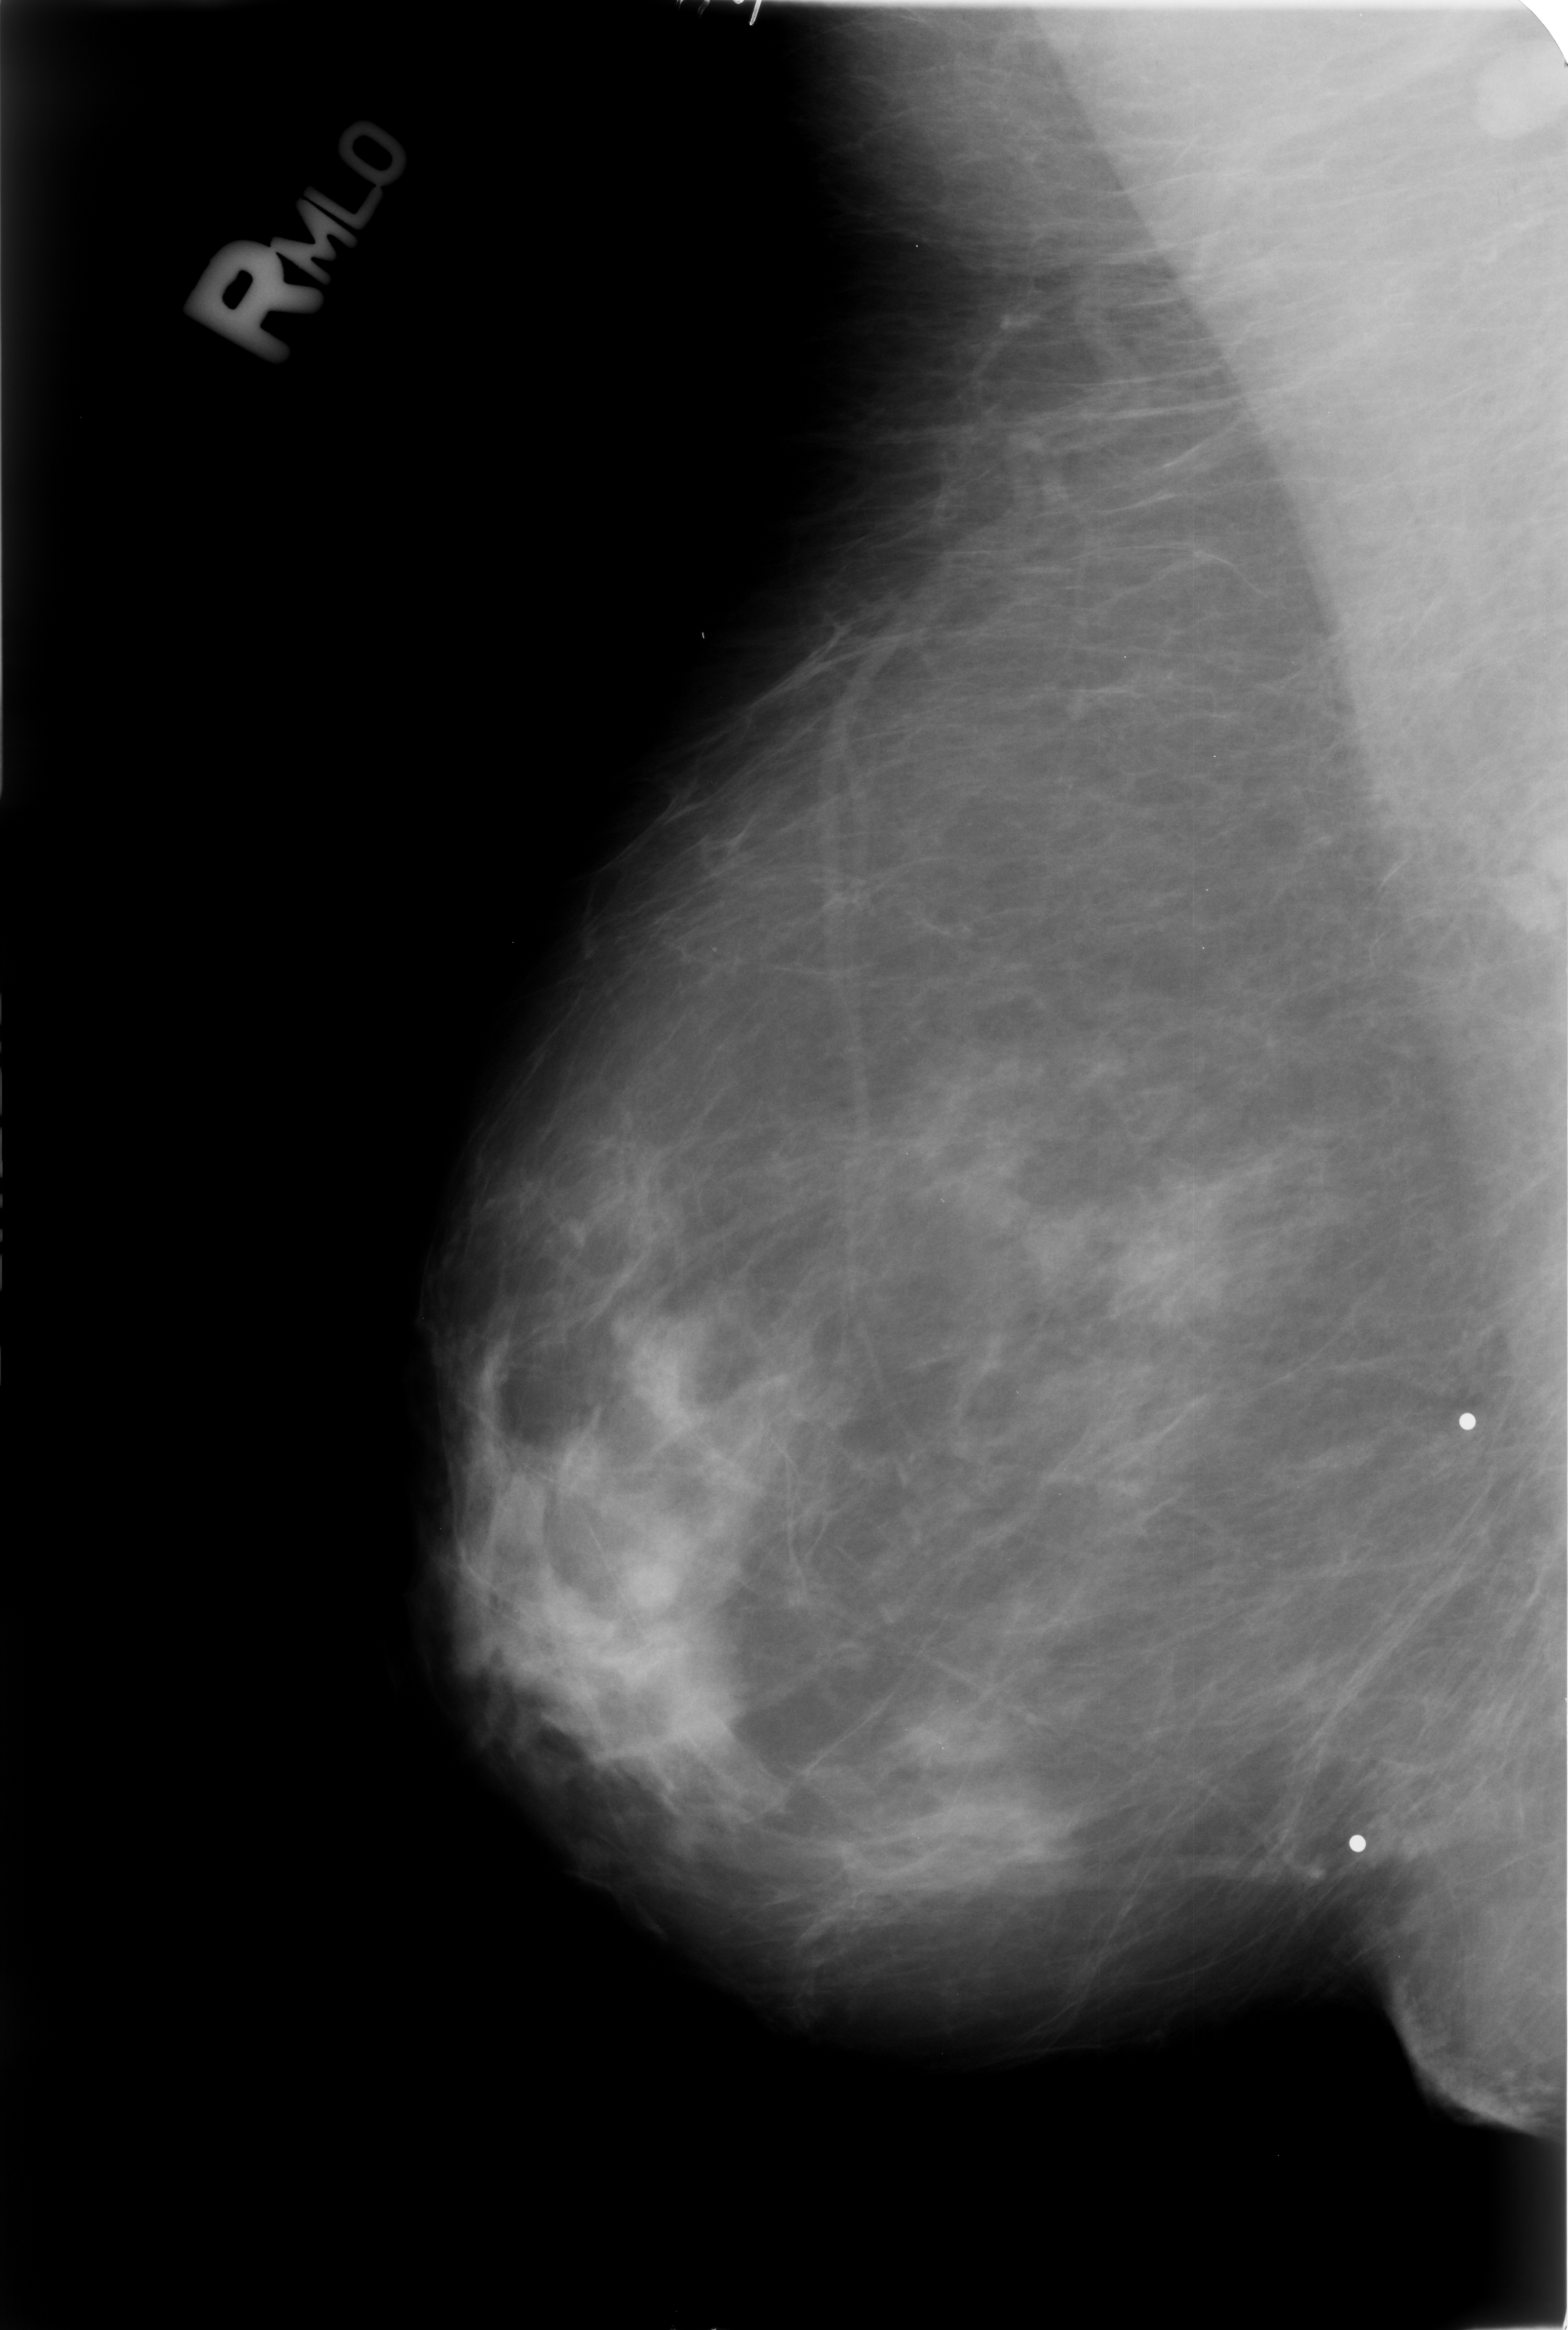
Scanned film-screen mammogram. Right breast. MLO view. Breast composition: scattered fibroglandular densities (BI-RADS density category 2 of 4). 1568 × 2330 image matrix.
Marked abnormalities (boxes around the expert regions of interest):
- calcifications, morphology punctate; BI-RADS assessment category 2; subtlety rating 3 on a 1 (subtle) to 5 (obvious) scale; outcome (as recorded, no biopsy): benign without callback (not worked up further): bounding box [x1, y1, x2, y2] px = [692, 927, 738, 978]